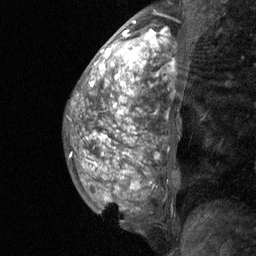
Breast MRI (dynamic contrast-enhanced), one sagittal slice; slice 25 of 64 in the series (ordered by position); dynamic contrast-enhanced study with each time point stored as its own series, time point 2 of 3 at this slice position (early post-contrast, ordered by acquisition time); 1.5 T; TE 4.8 ms, TR 27 ms; 256 × 256 image matrix, field of view 180 × 180 mm. Female patient, age 36 years. From the clinical record (not read from this slice): setting: breast cancer imaged before/during neoadjuvant chemotherapy; receptor status: HR-positive, HER2-negative.
Annotated regions visible in this slice (semi-automatic segmentation, software-assisted and operator-edited):
- analysis volume of interest (the breast-tissue region the enhancement analysis was run in; not a lesion): bounding box (x1, y1, x2, y2) in pixels: (67, 12, 191, 235)
- tumour enhancement mask (voxels above the 90 % enhancement threshold inside the analysis volume of interest): (90, 22, 167, 165)